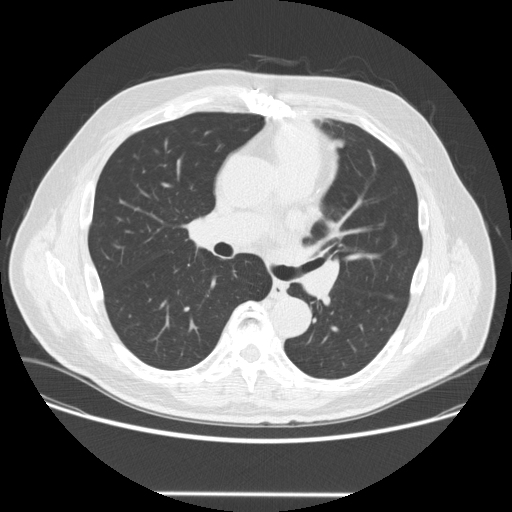
Low-dose screening chest CT, one axial slice. Position 153 of 253 along the scan axis. Lung window (W 1500 / L -600 HU). 2.5 mm slice thickness. 512 × 512 image matrix.
Annotated regions visible in this slice (manually delineated by an expert):
- lesion 1 (tumor, upper lobe of left lung): bounding box <329,223,339,235> (left, top, right, bottom; pixels)